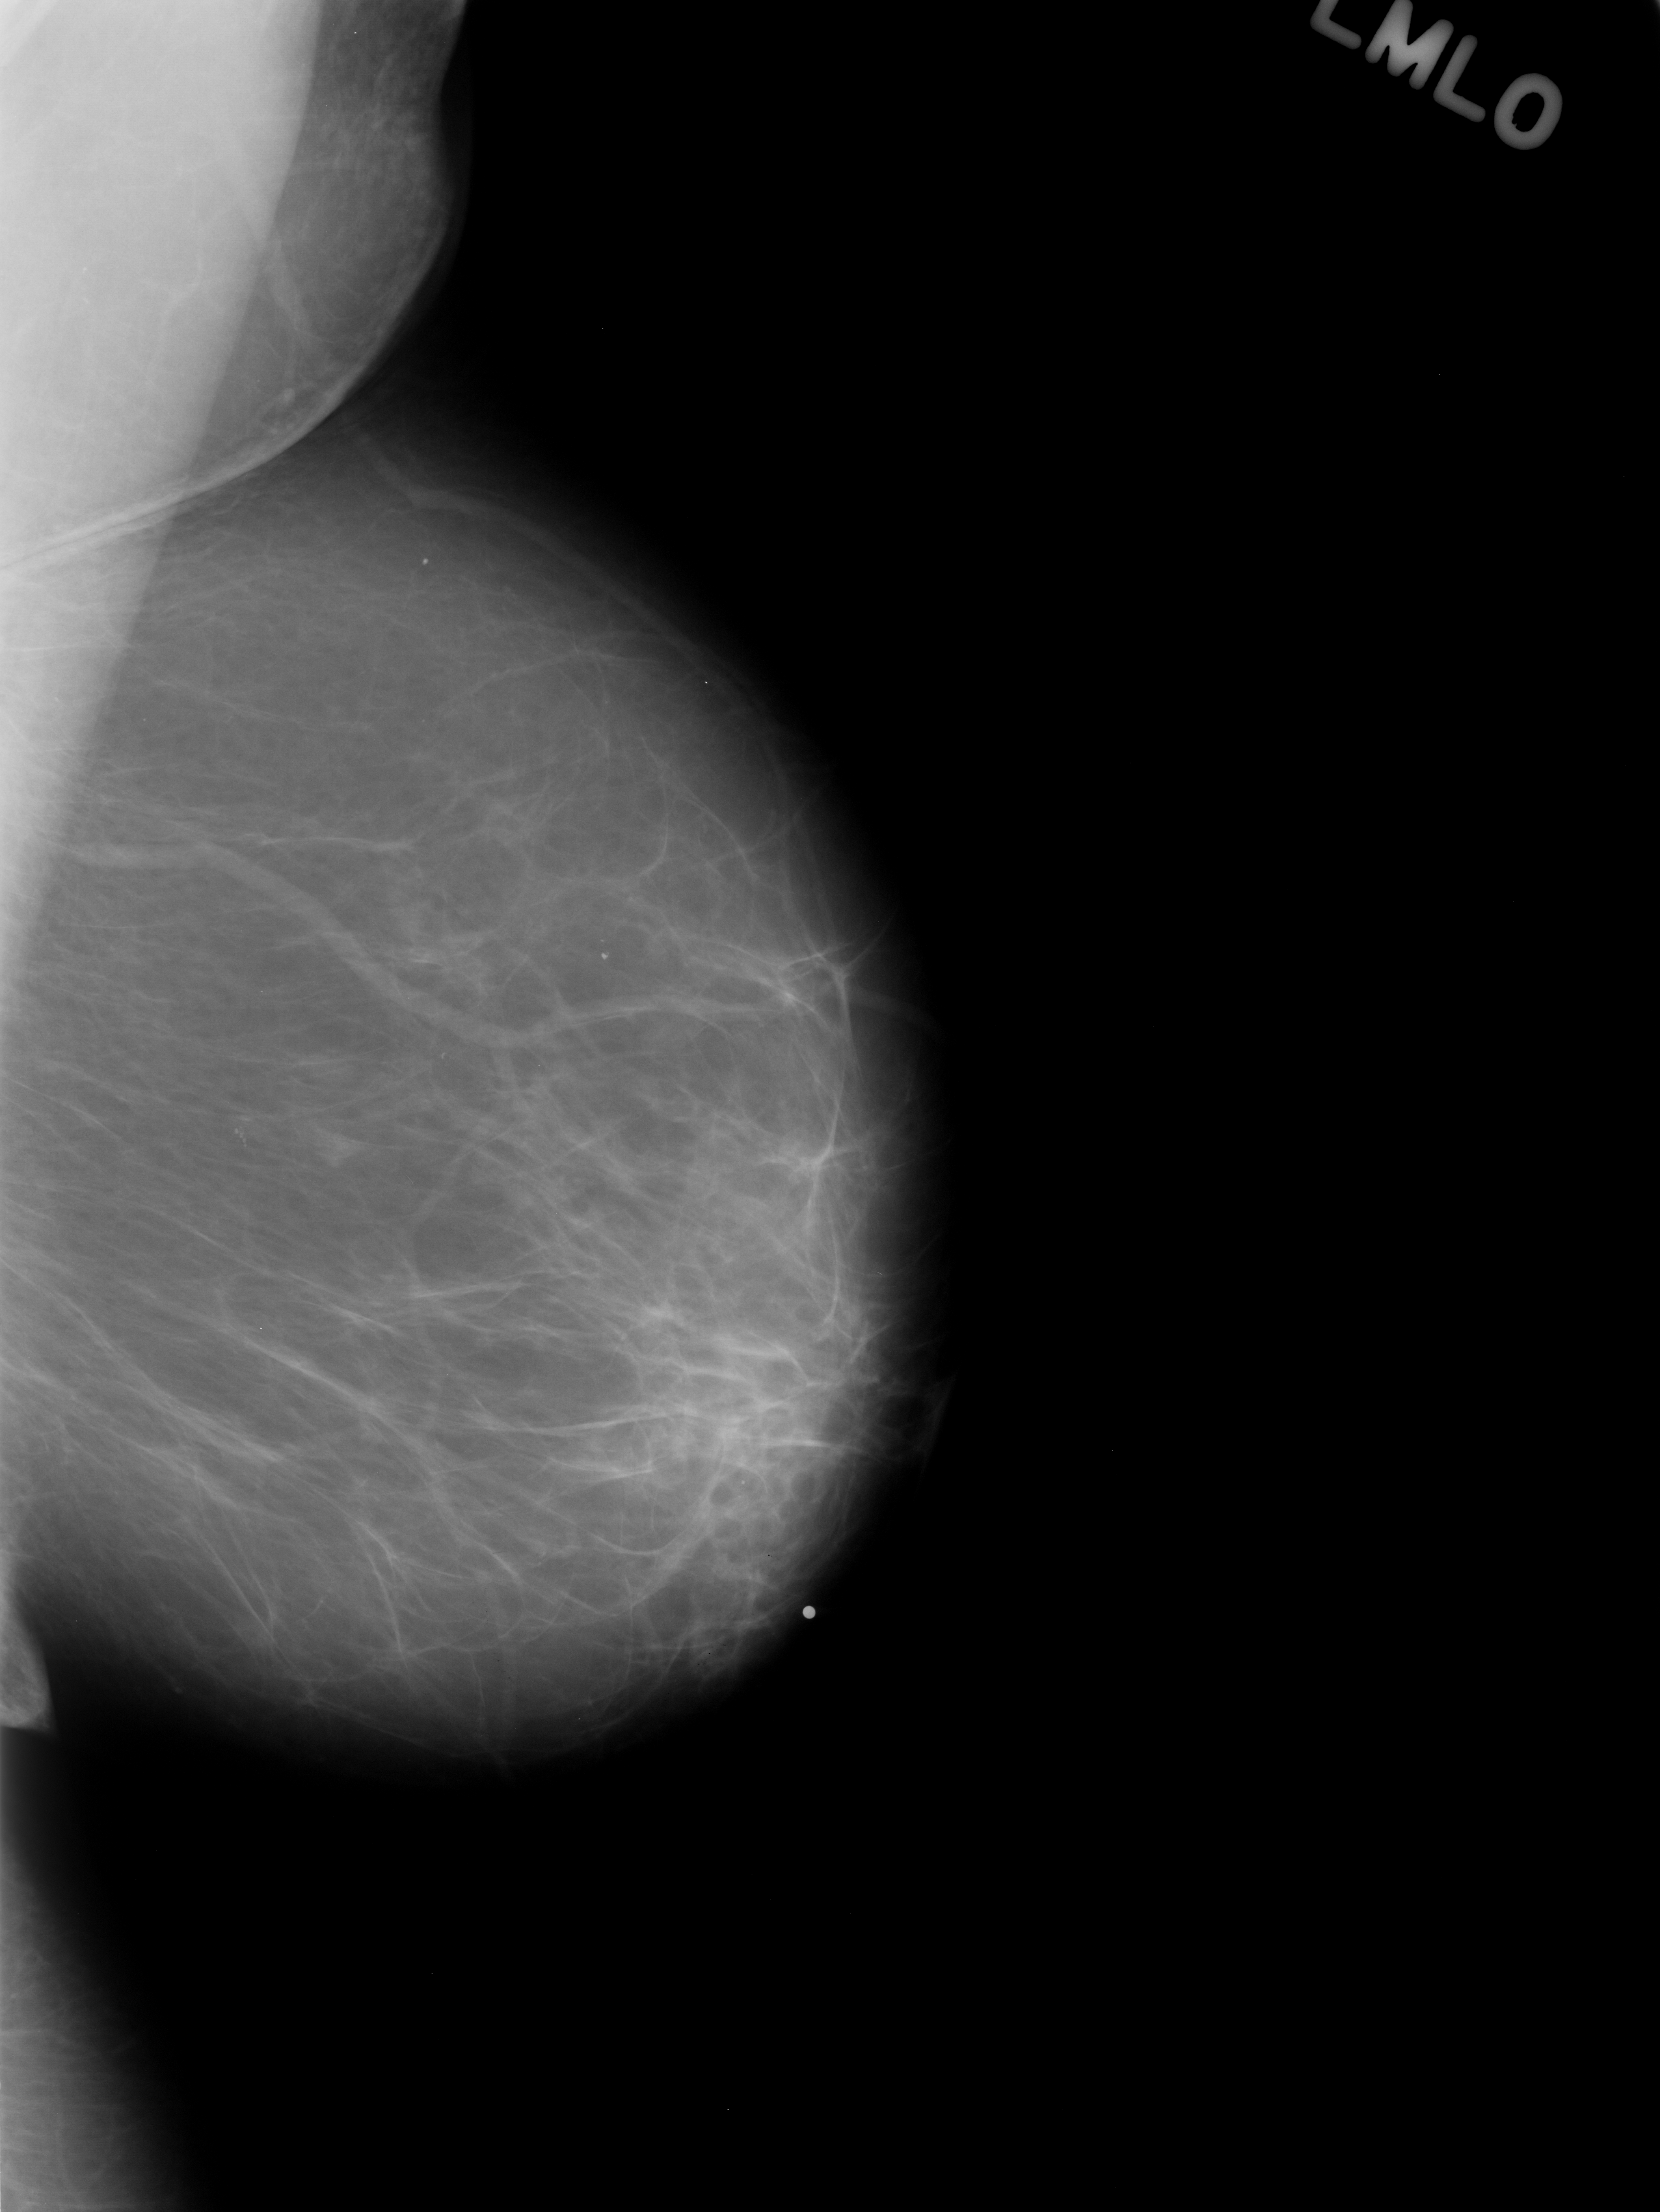
Scanned film-screen mammogram, left breast, mediolateral oblique (MLO) view, BI-RADS breast density category 1 (scale 1–4).
Abnormality record for this image: mass, shape focal asymmetric density, margins ill defined; BI-RADS assessment category 3; subtlety rating 5 on a 1 (subtle) to 5 (obvious) scale; pathology result (as recorded, not read from the image): benign.